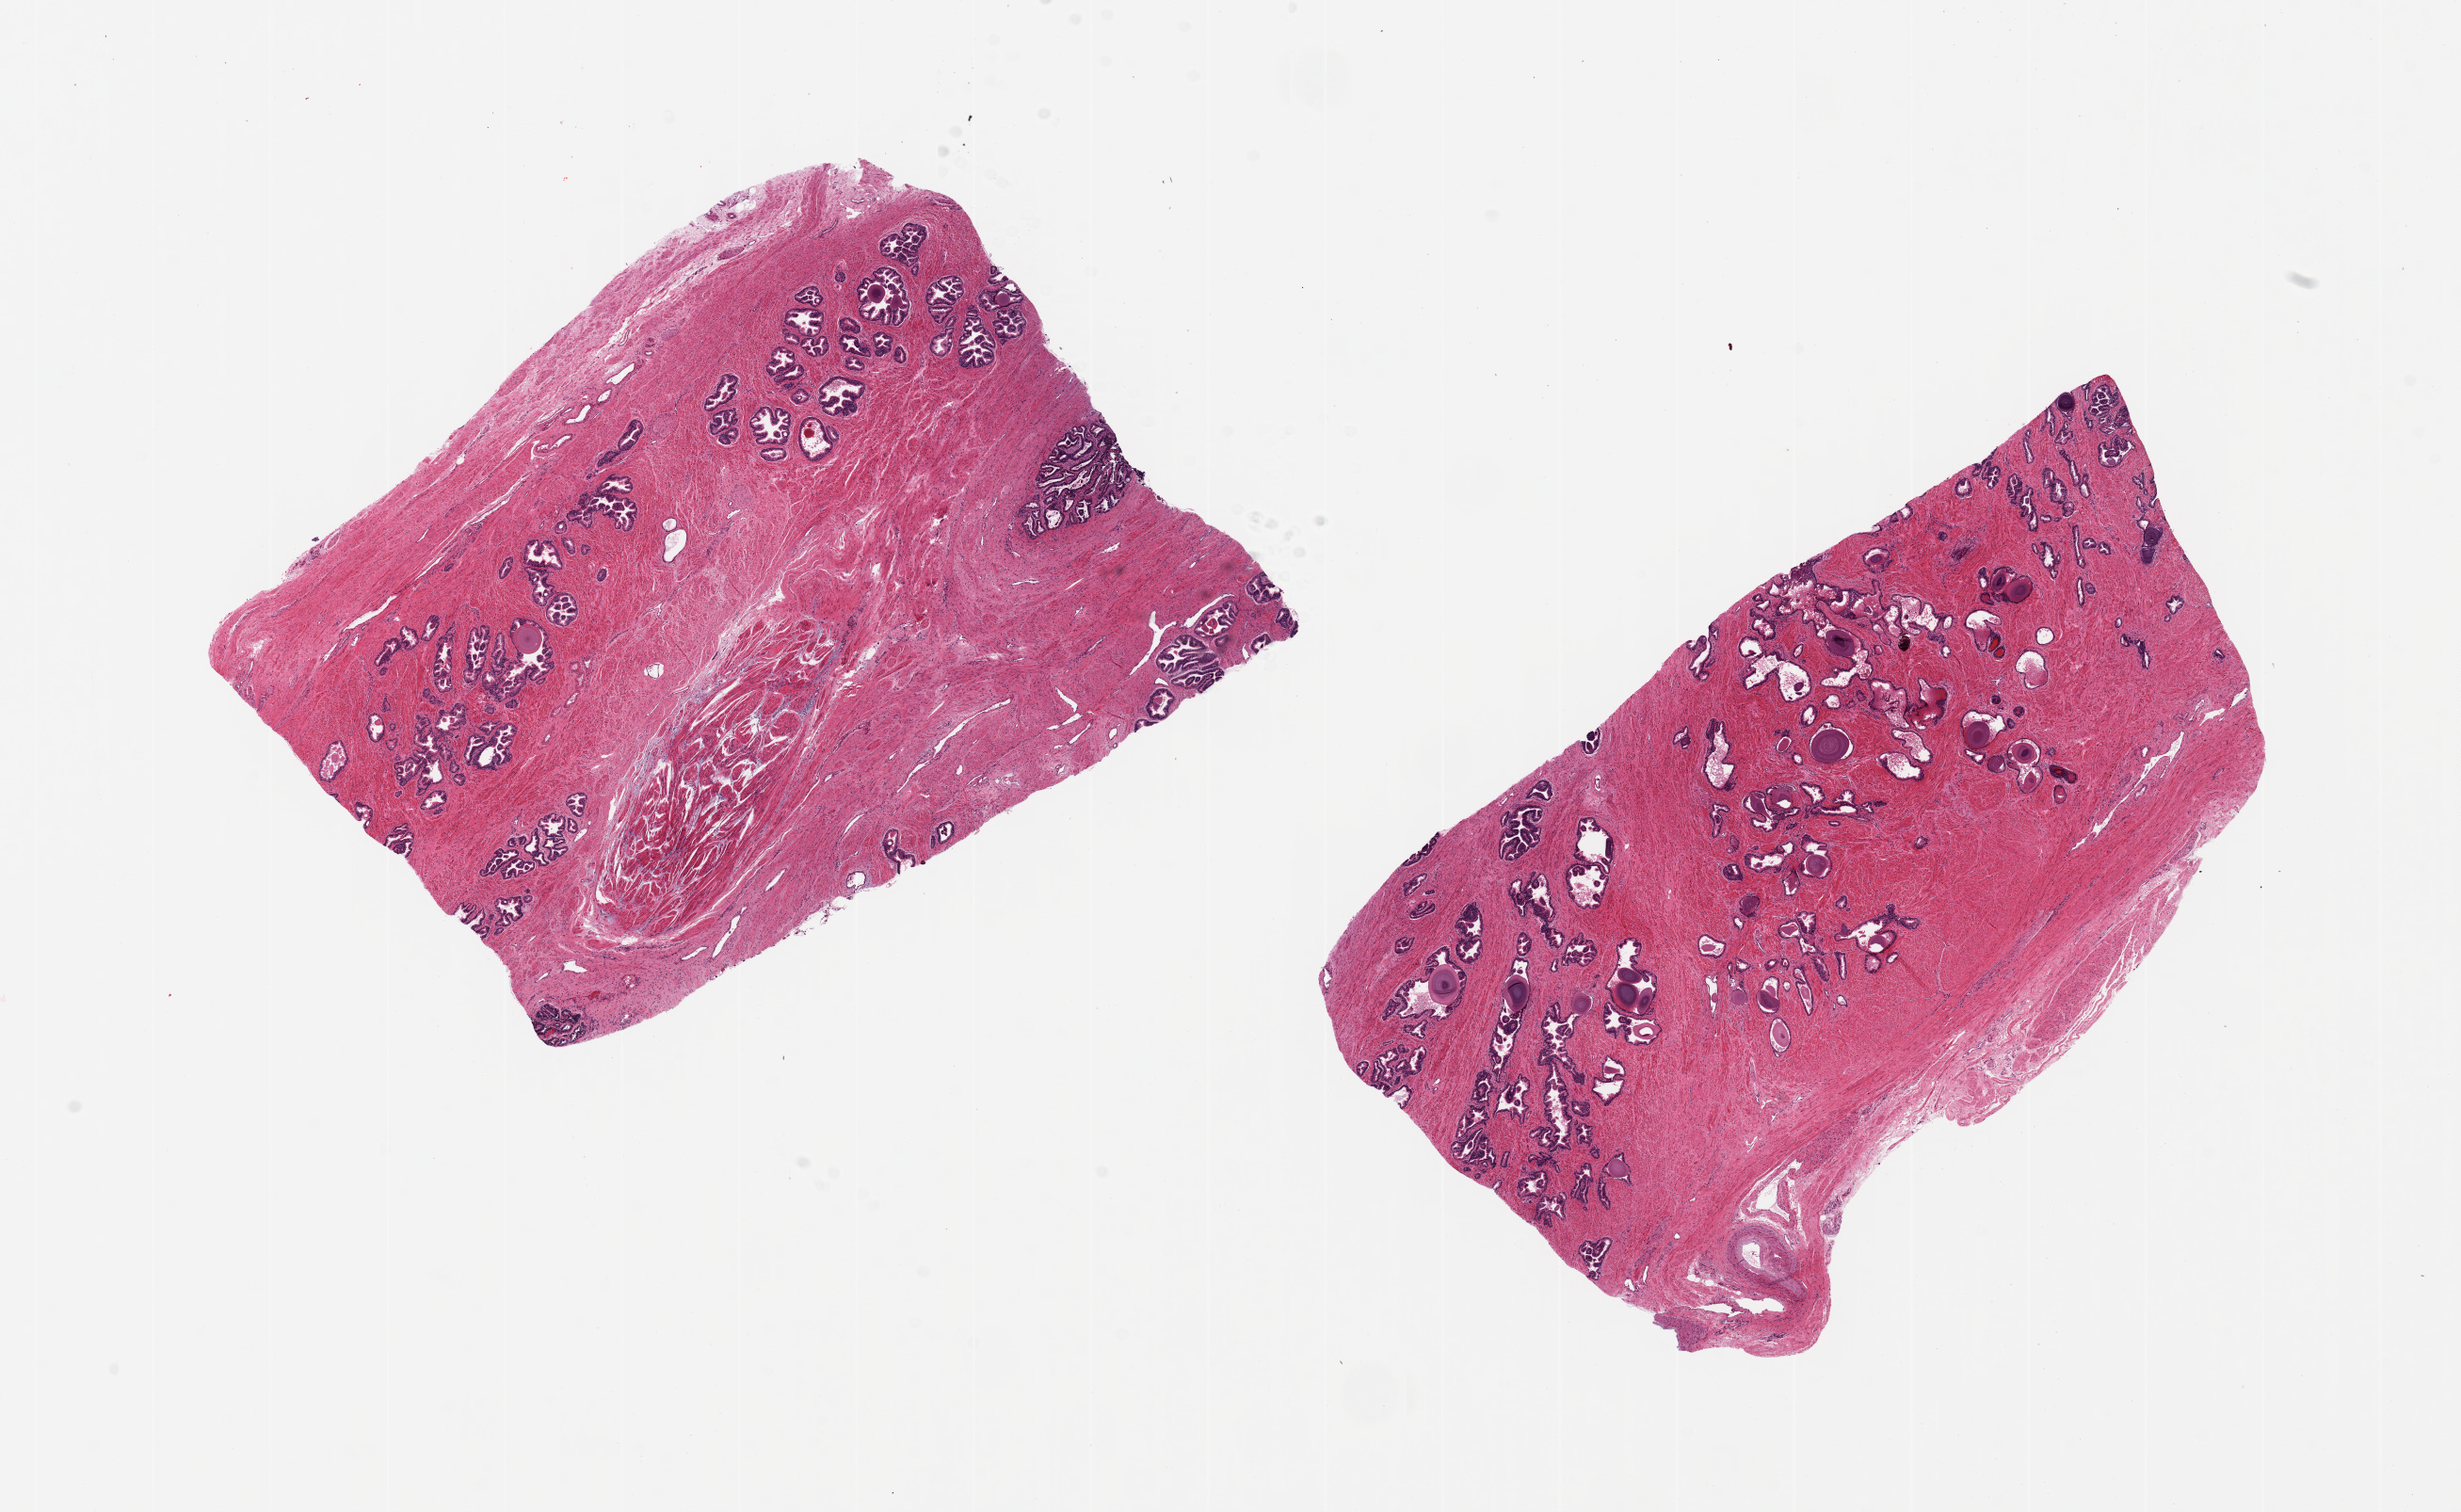
H&E whole-slide image, shown as a low-resolution overview of the whole scanned area (about 20.7 x 12.7 mm, from a 20x scan); PAXgene-fixed, paraffin-embedded tissue; target tissue: prostate; tissue donor sample. Donor sex: male.
Reviewer comment on this tissue sample: 2 pieces, 7x6 & 9x5mm; Well preserved, focal papillary hyperplasia; focus of seminal vesicle 1x0.7mm in 1 piece.